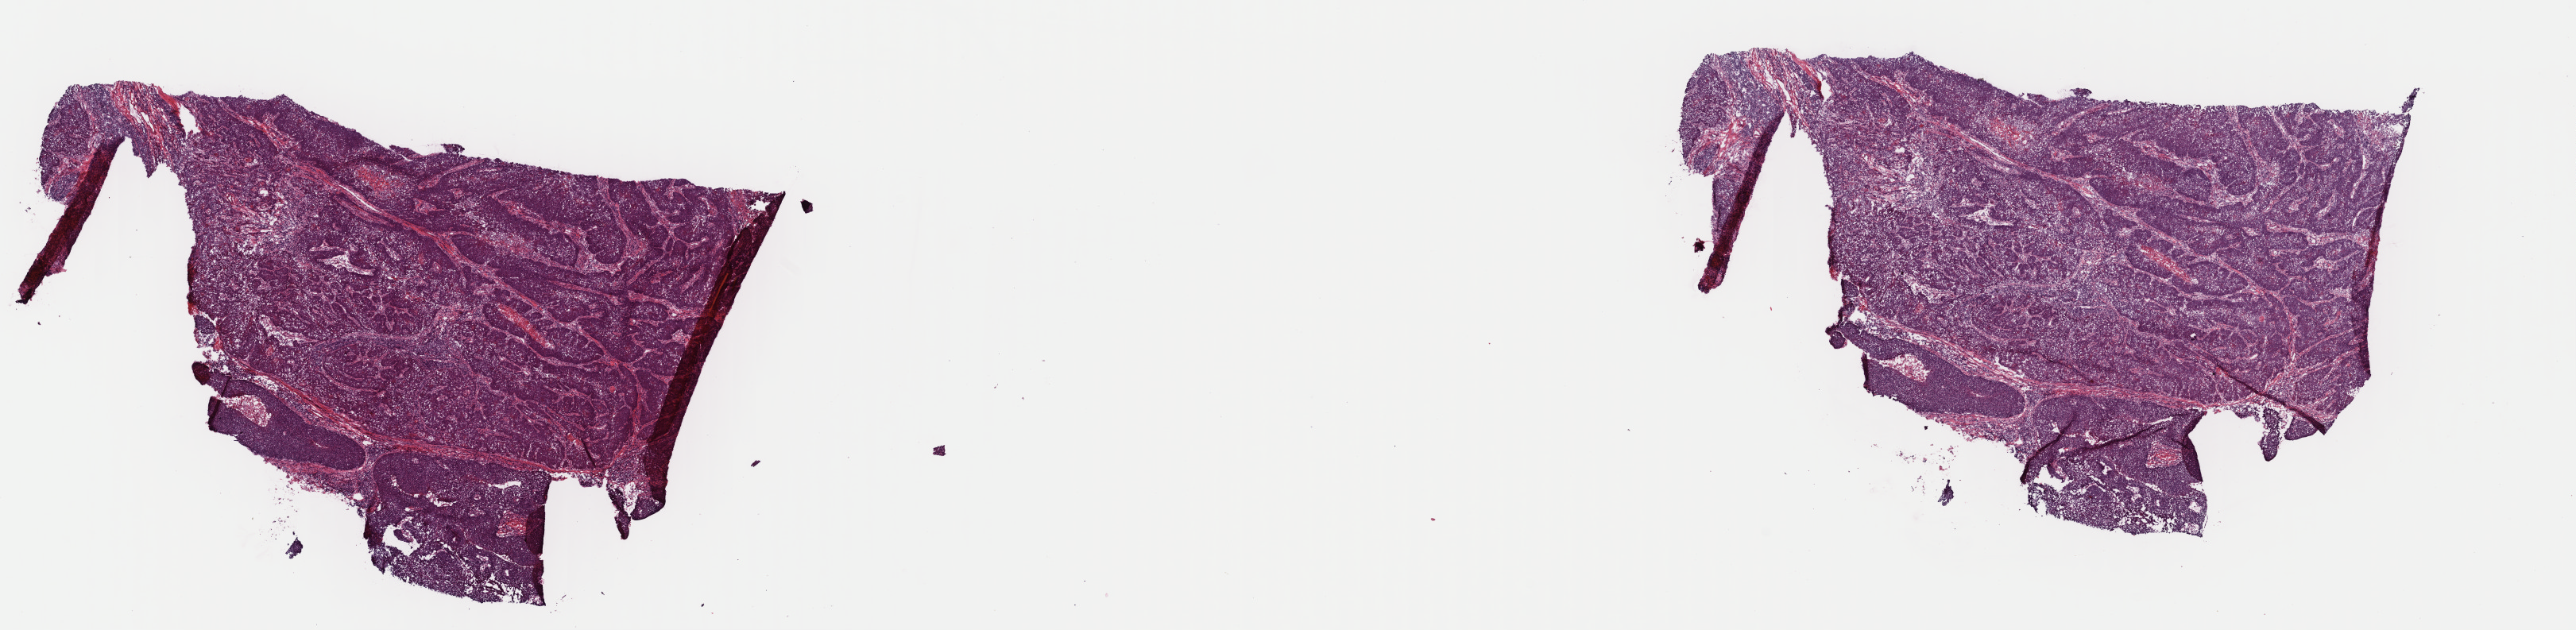
Whole-slide histology image, H&E, low-resolution overview of the scanned area, about 25.6 x 6.3 mm (from a 40x scan); frozen section from the top of the tissue portion; primary tumour sample from the head and neck. Male, age 63 years at initial diagnosis. Histologic grade: G3 (poorly differentiated). Composition of this section per pathologist review: tumour cells 80%, tumour nuclei 90%, normal cells 0%, stromal cells 18%, necrosis 2%. Inflammatory infiltration, as recorded: lymphocyte infiltration 6%, monocyte infiltration 2%, neutrophil infiltration 1%.
Laterality: left. AJCC pathologic stage: IVA (7th edition). Diagnosis: Squamous cell carcinoma, large cell, nonkeratinizing, NOS (tonsil, NOS).